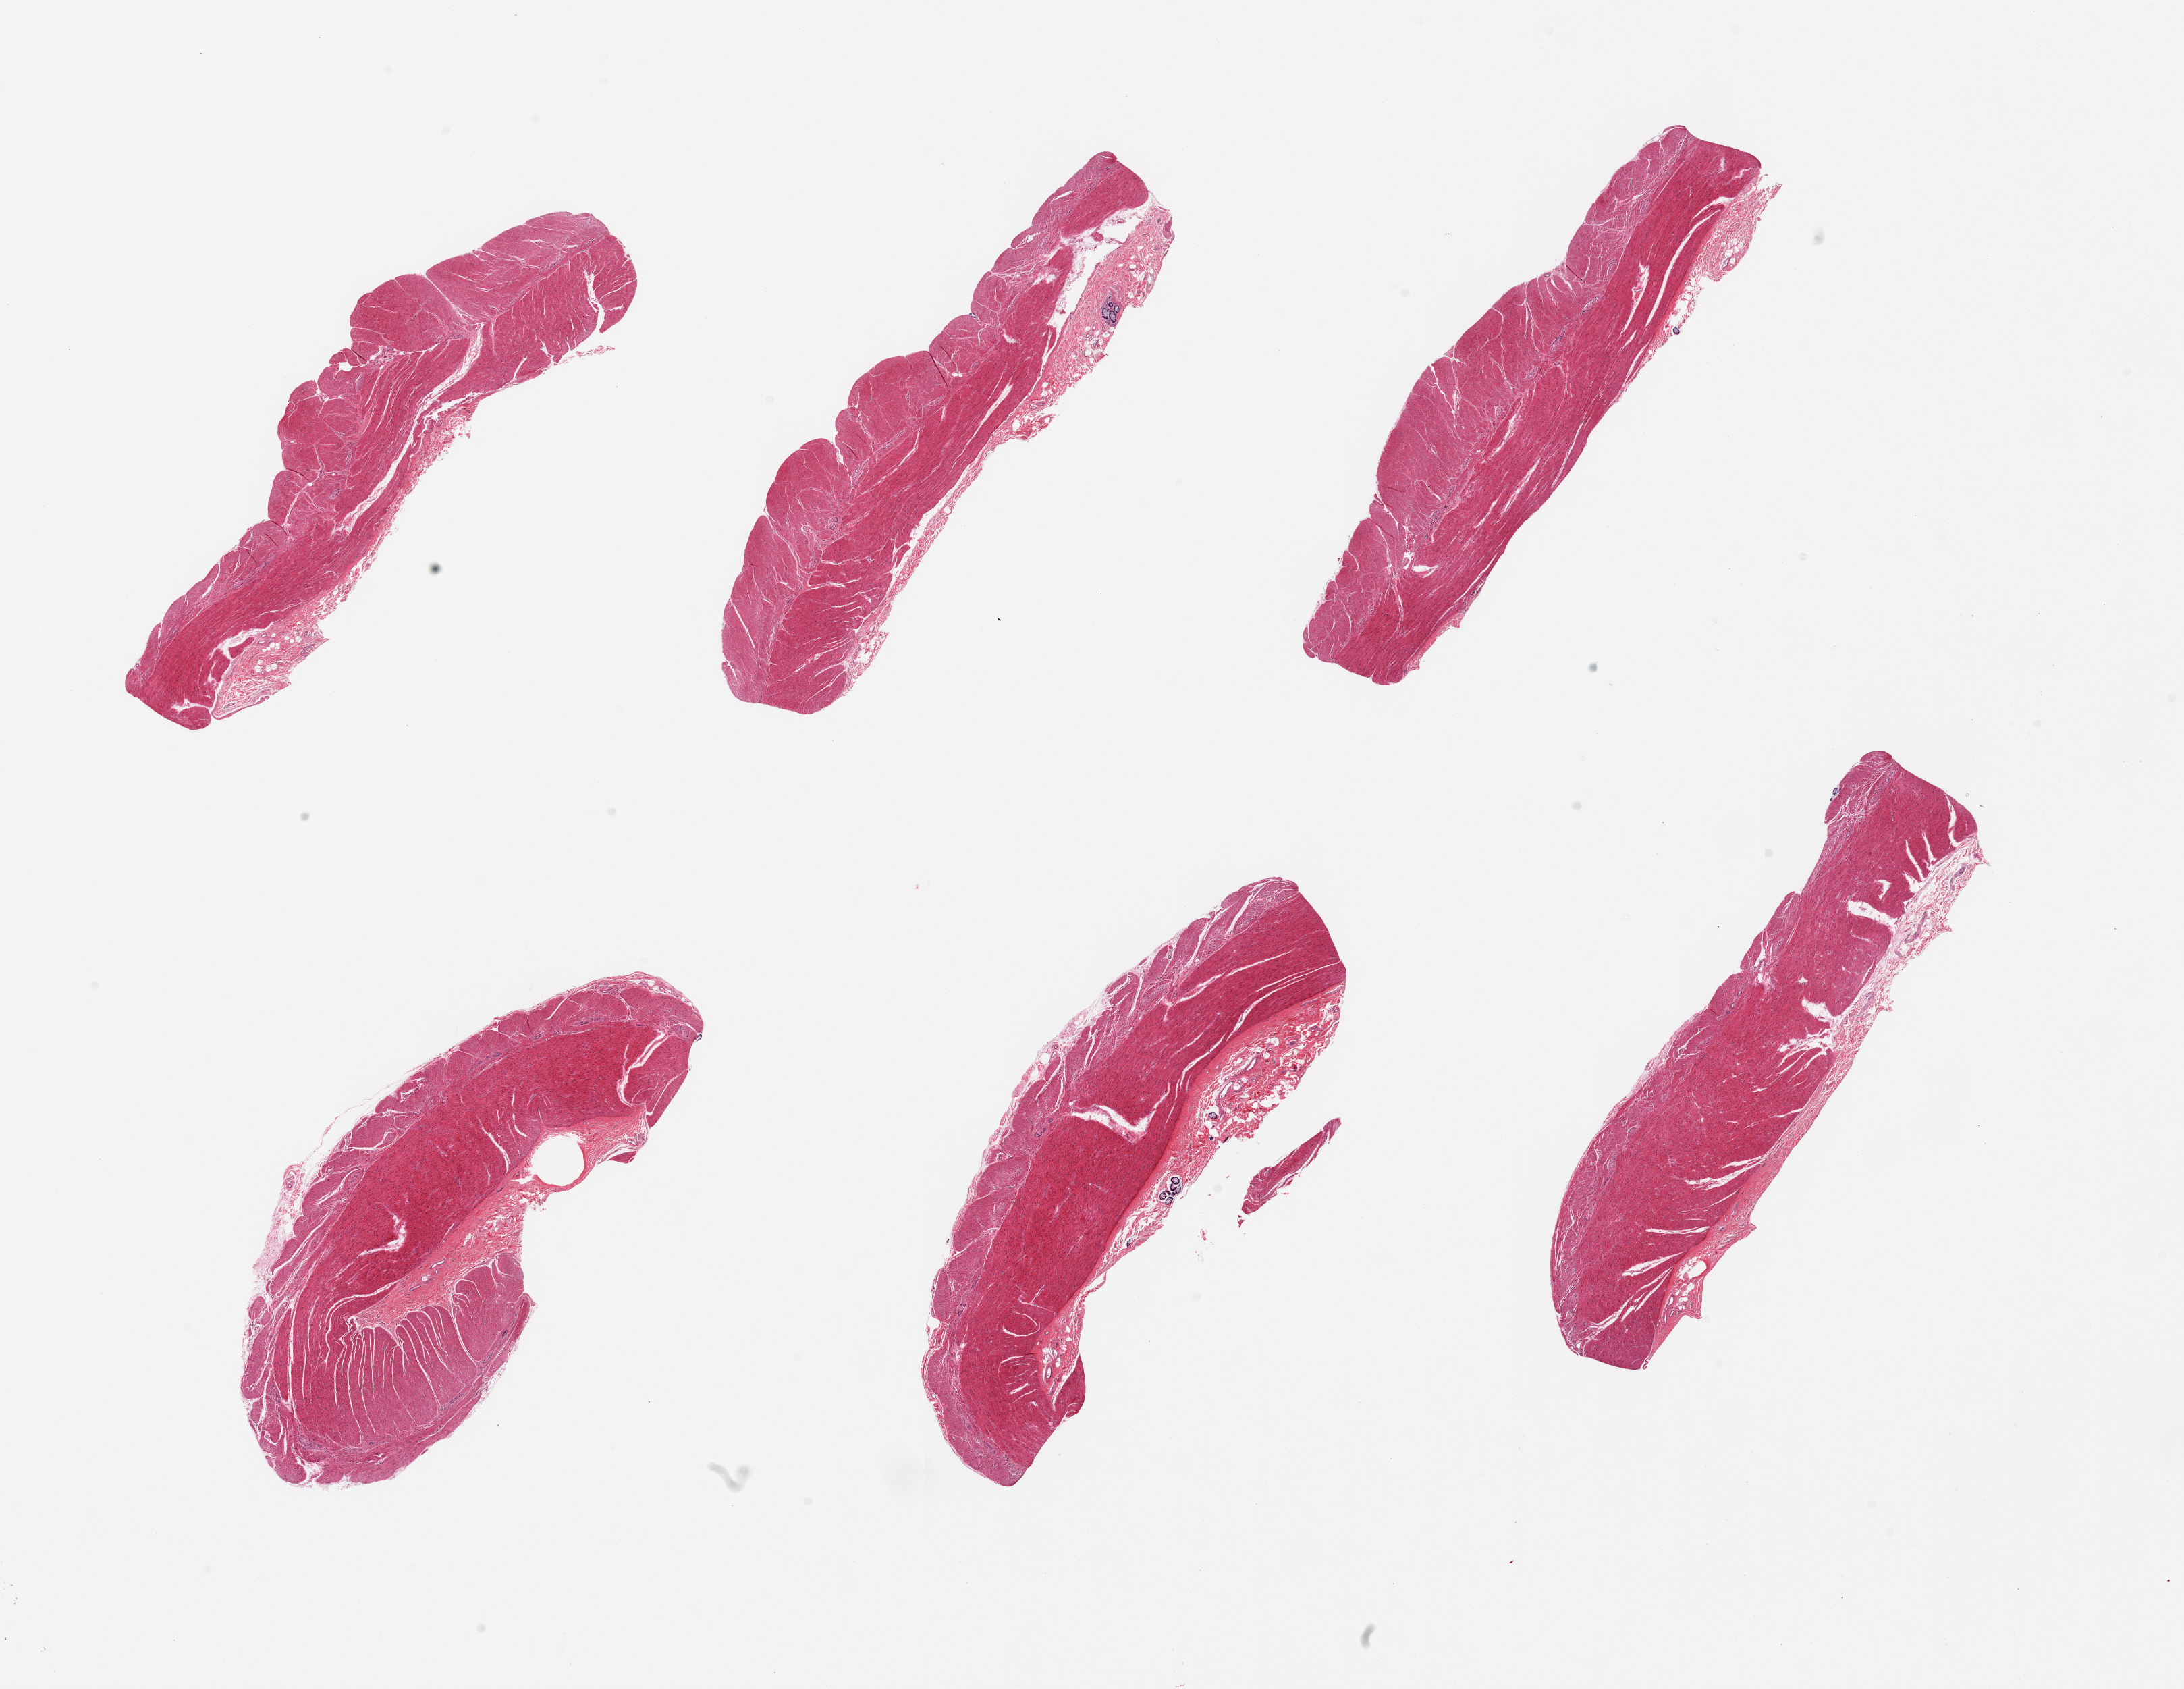
Whole-slide image, haematoxylin and eosin stain, low-resolution overview of the scanned area, about 25.6 x 19.8 mm; PAXgene-fixed paraffin-embedded (PFPE) section; section of sigmoid colon (target tissue); tissue donor sample. Male donor.
- pathologist's review note for this sample: 6 pieces; well dissected except for occasional small foci of mucosa